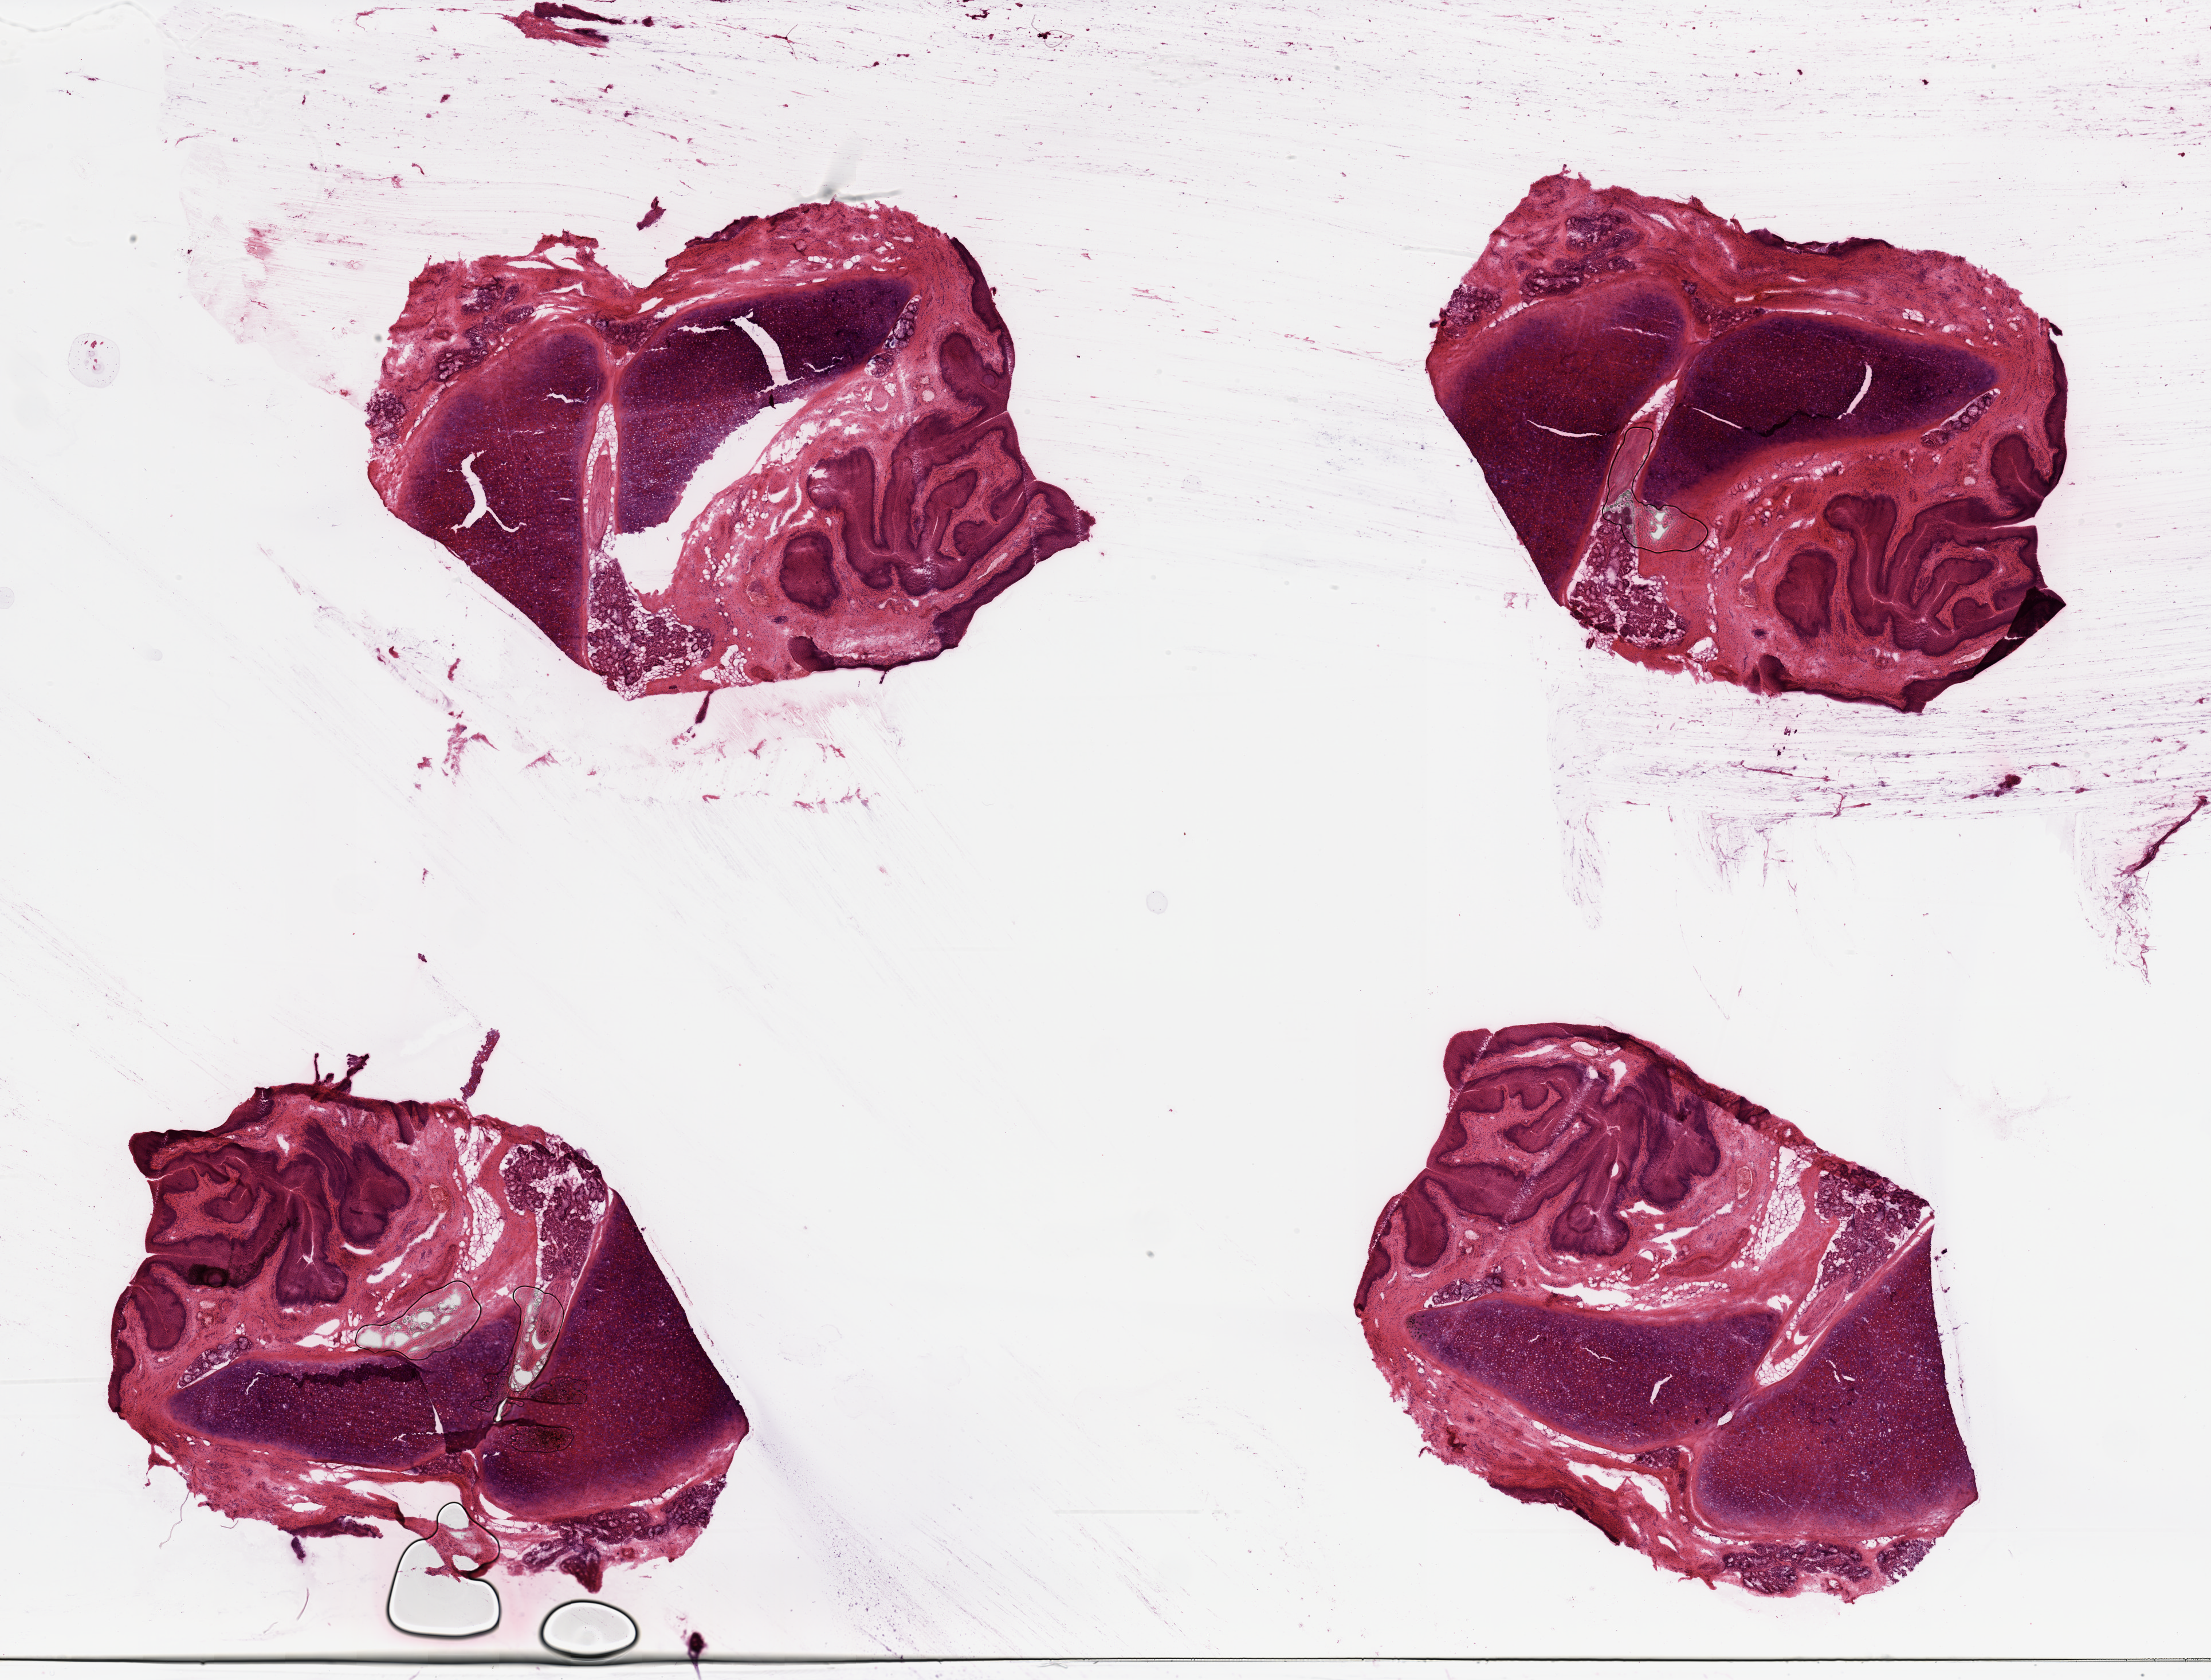
Whole-slide histology image, Hematoxylin and eosin (H&E) stained, whole scanned area (about 30.5 x 23.2 mm, acquisition: 20x scan) shown as a low-resolution overview. Normal (non-tumour) tissue sample, sampled site: larynx. 50-year-old male patient.
• this section: normal (non-tumour) tissue from the same patient
• patient diagnosis: Squamous cell carcinoma, NOS (larynx, NOS)